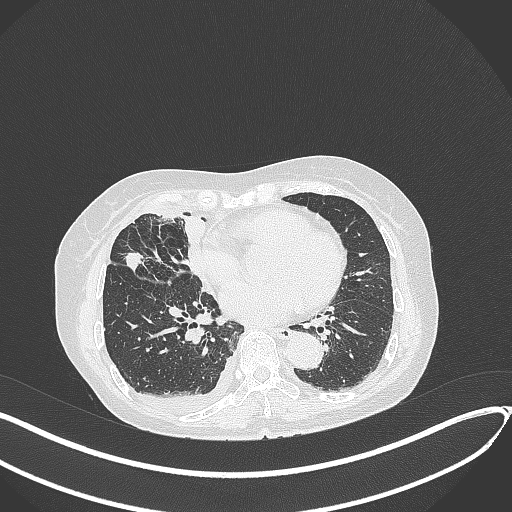
Chest CT, one axial slice. Reconstruction kernel B70f. Lung window (W 1500 / L -600 HU). 1 mm slice thickness. 512 × 512 image matrix, field of view 400 × 400 mm. Female patient, age 75 years. From the clinical record (not read from this slice): clinical TNM (as recorded): T2a N3 M0.
Outlined on this slice (rectangle marked by the reading radiologist):
- lung tumour (recorded histology: adenocarcinoma): bounding box <120,250,148,273> (left, top, right, bottom; pixels)